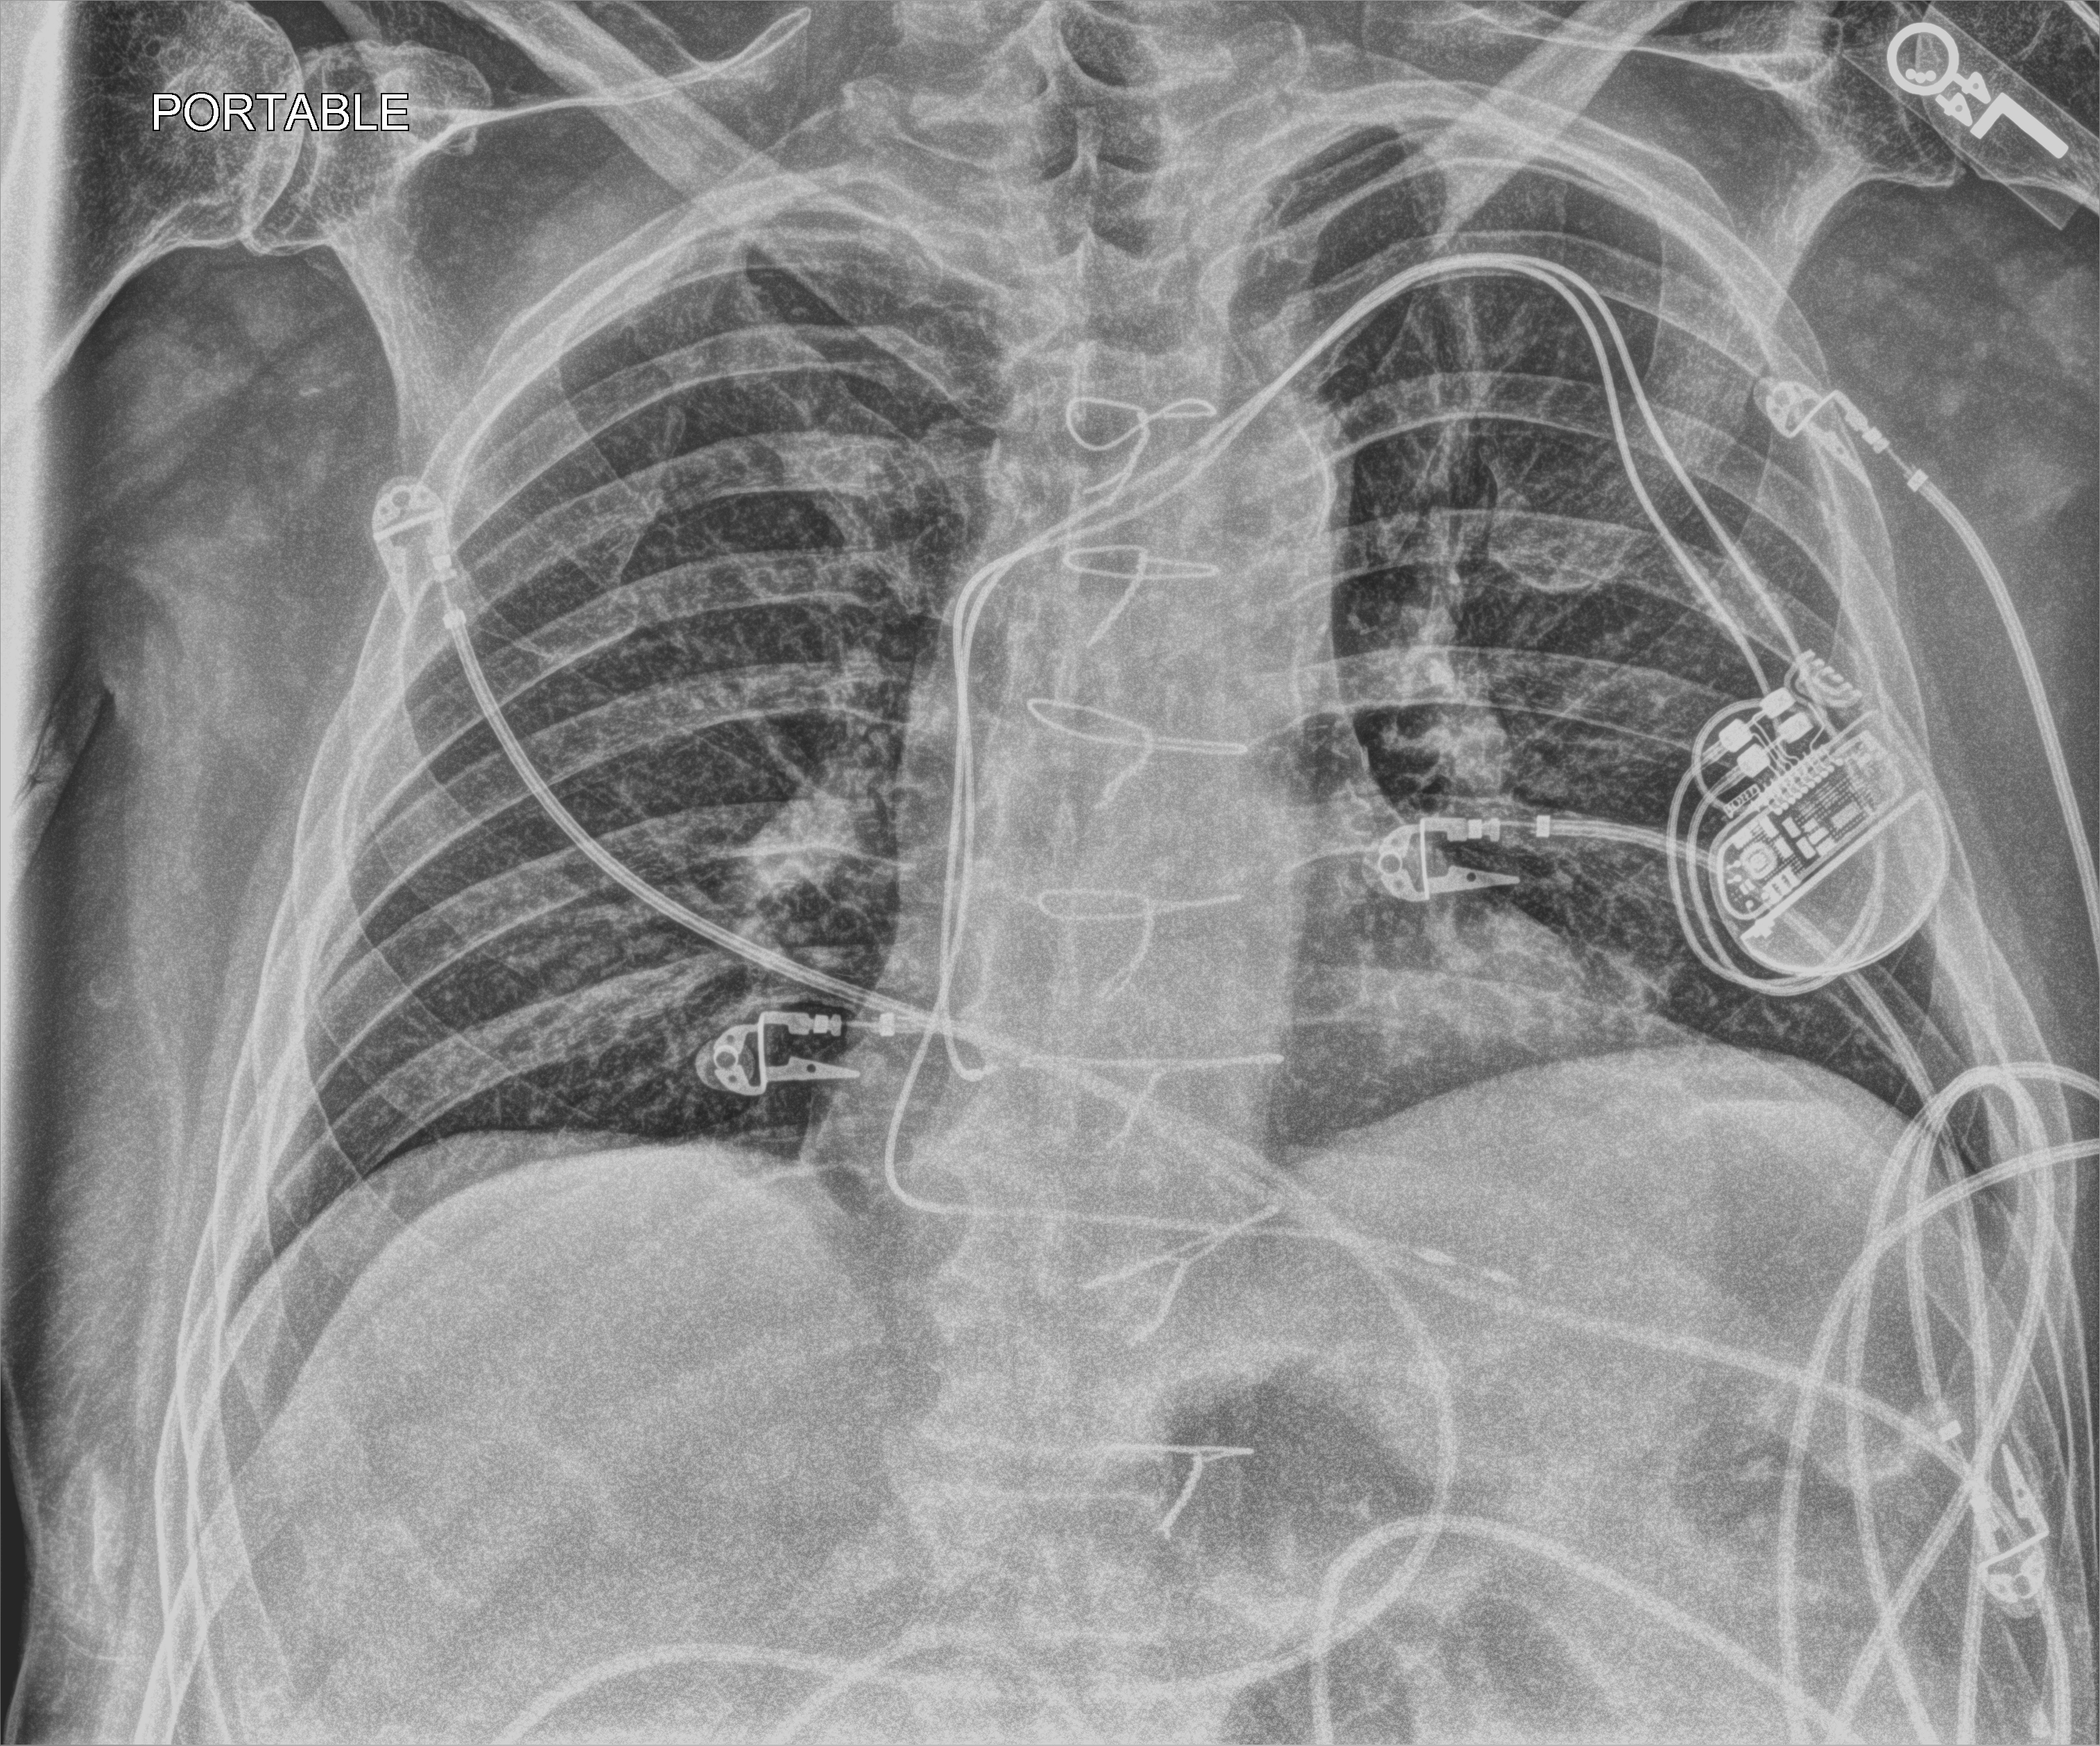
Bedside chest radiograph (computed radiography); anteroposterior (AP) projection. Patient hospitalised with COVID-19; male, aged 75–90 years.
Hospital-stay facts (about this admission, not read from this image; timing relative to this image not recorded):
- admitted to intensive care during this hospital stay: no